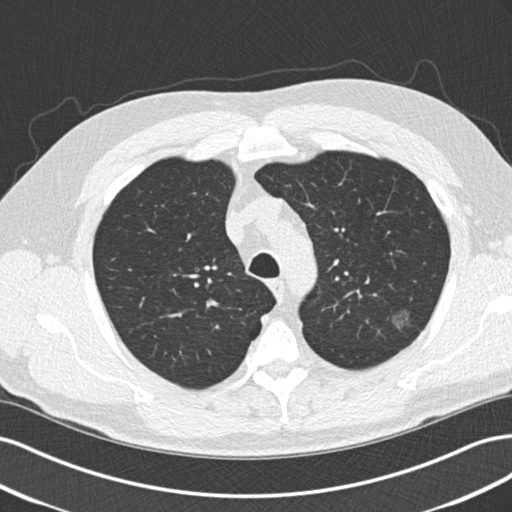
Low-dose screening chest CT, one axial slice; slice 164 of 209 in the series (ordered by position); lung window (W 1500 / L -600 HU); 2 mm slice thickness; 512 × 512 image matrix, field of view 360 × 360 mm.
Structures marked on this image (outlined manually by an expert reader):
- lesion 1 (tumor, upper lobe of left lung): bounding box (x1, y1, x2, y2) in pixels: (392, 311, 409, 327)